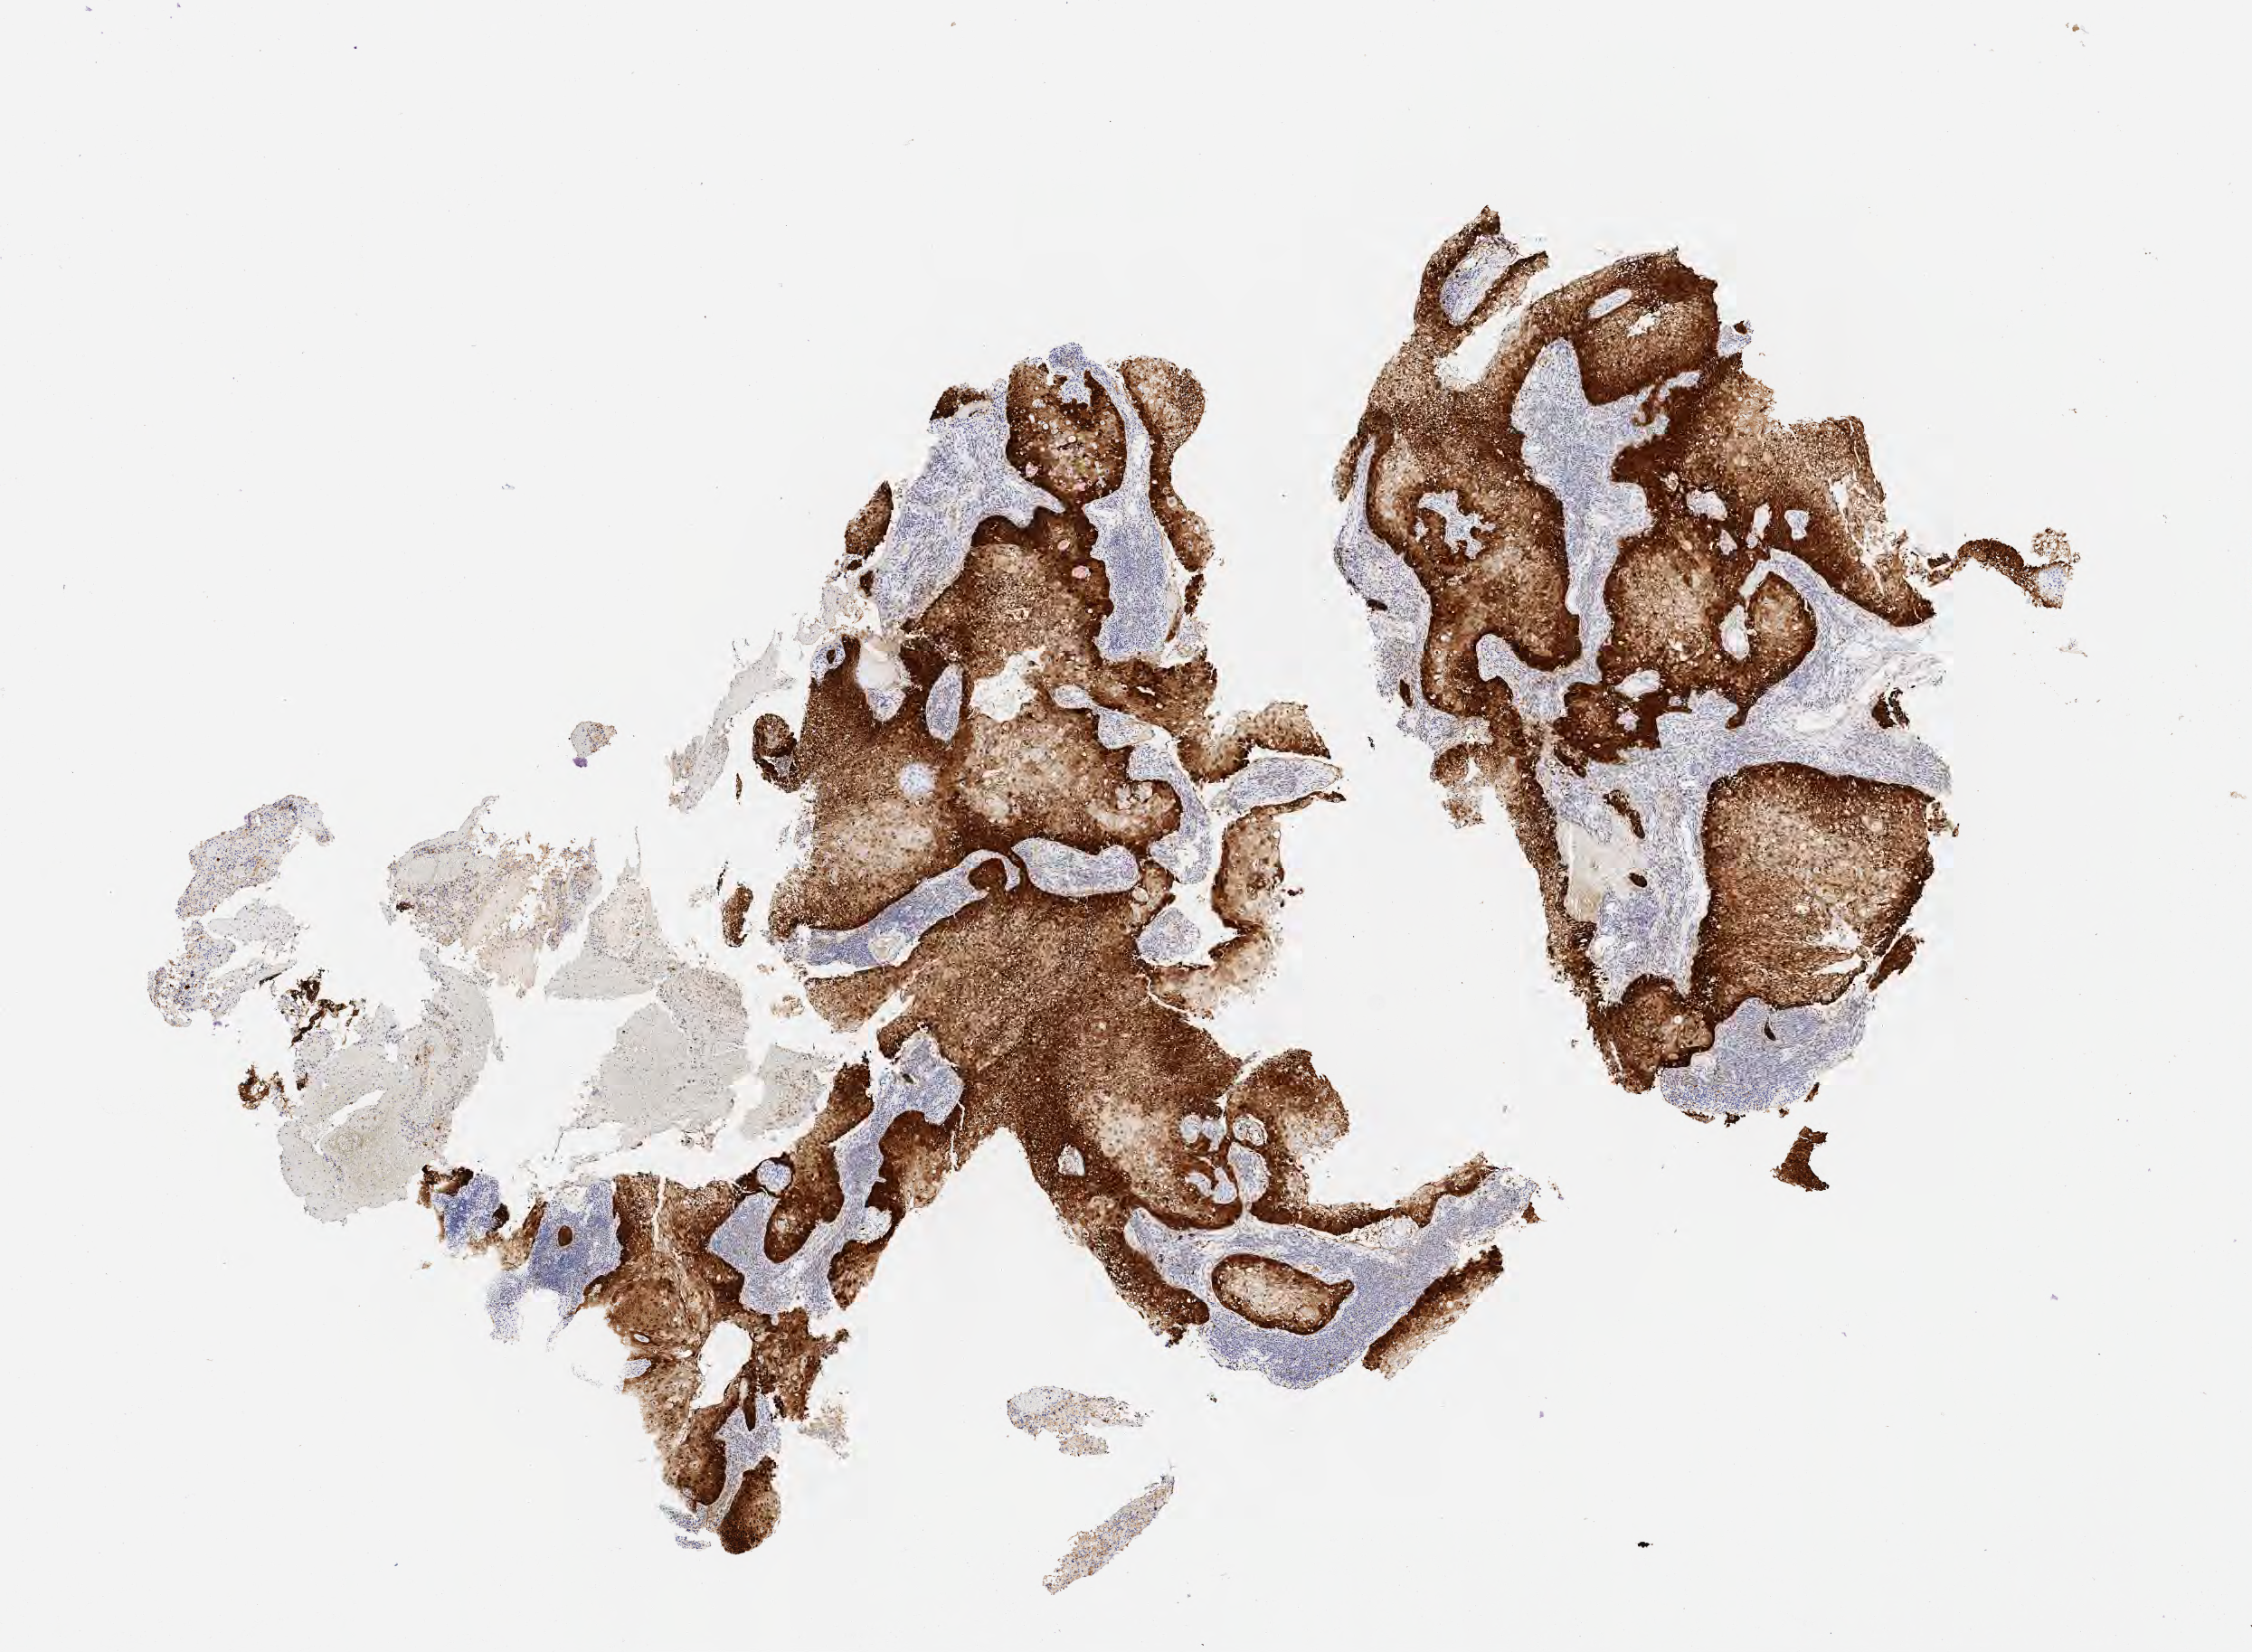
IHC for p16 (p16INK4a), whole-slide image, a low-resolution overview of the entire scanned area, about 10.1 x 7.4 mm; tumor tissue; site: cervix. Patient female; aged 43.
* histologic diagnosis: Squamous cell carcinoma, keratinizing, NOS